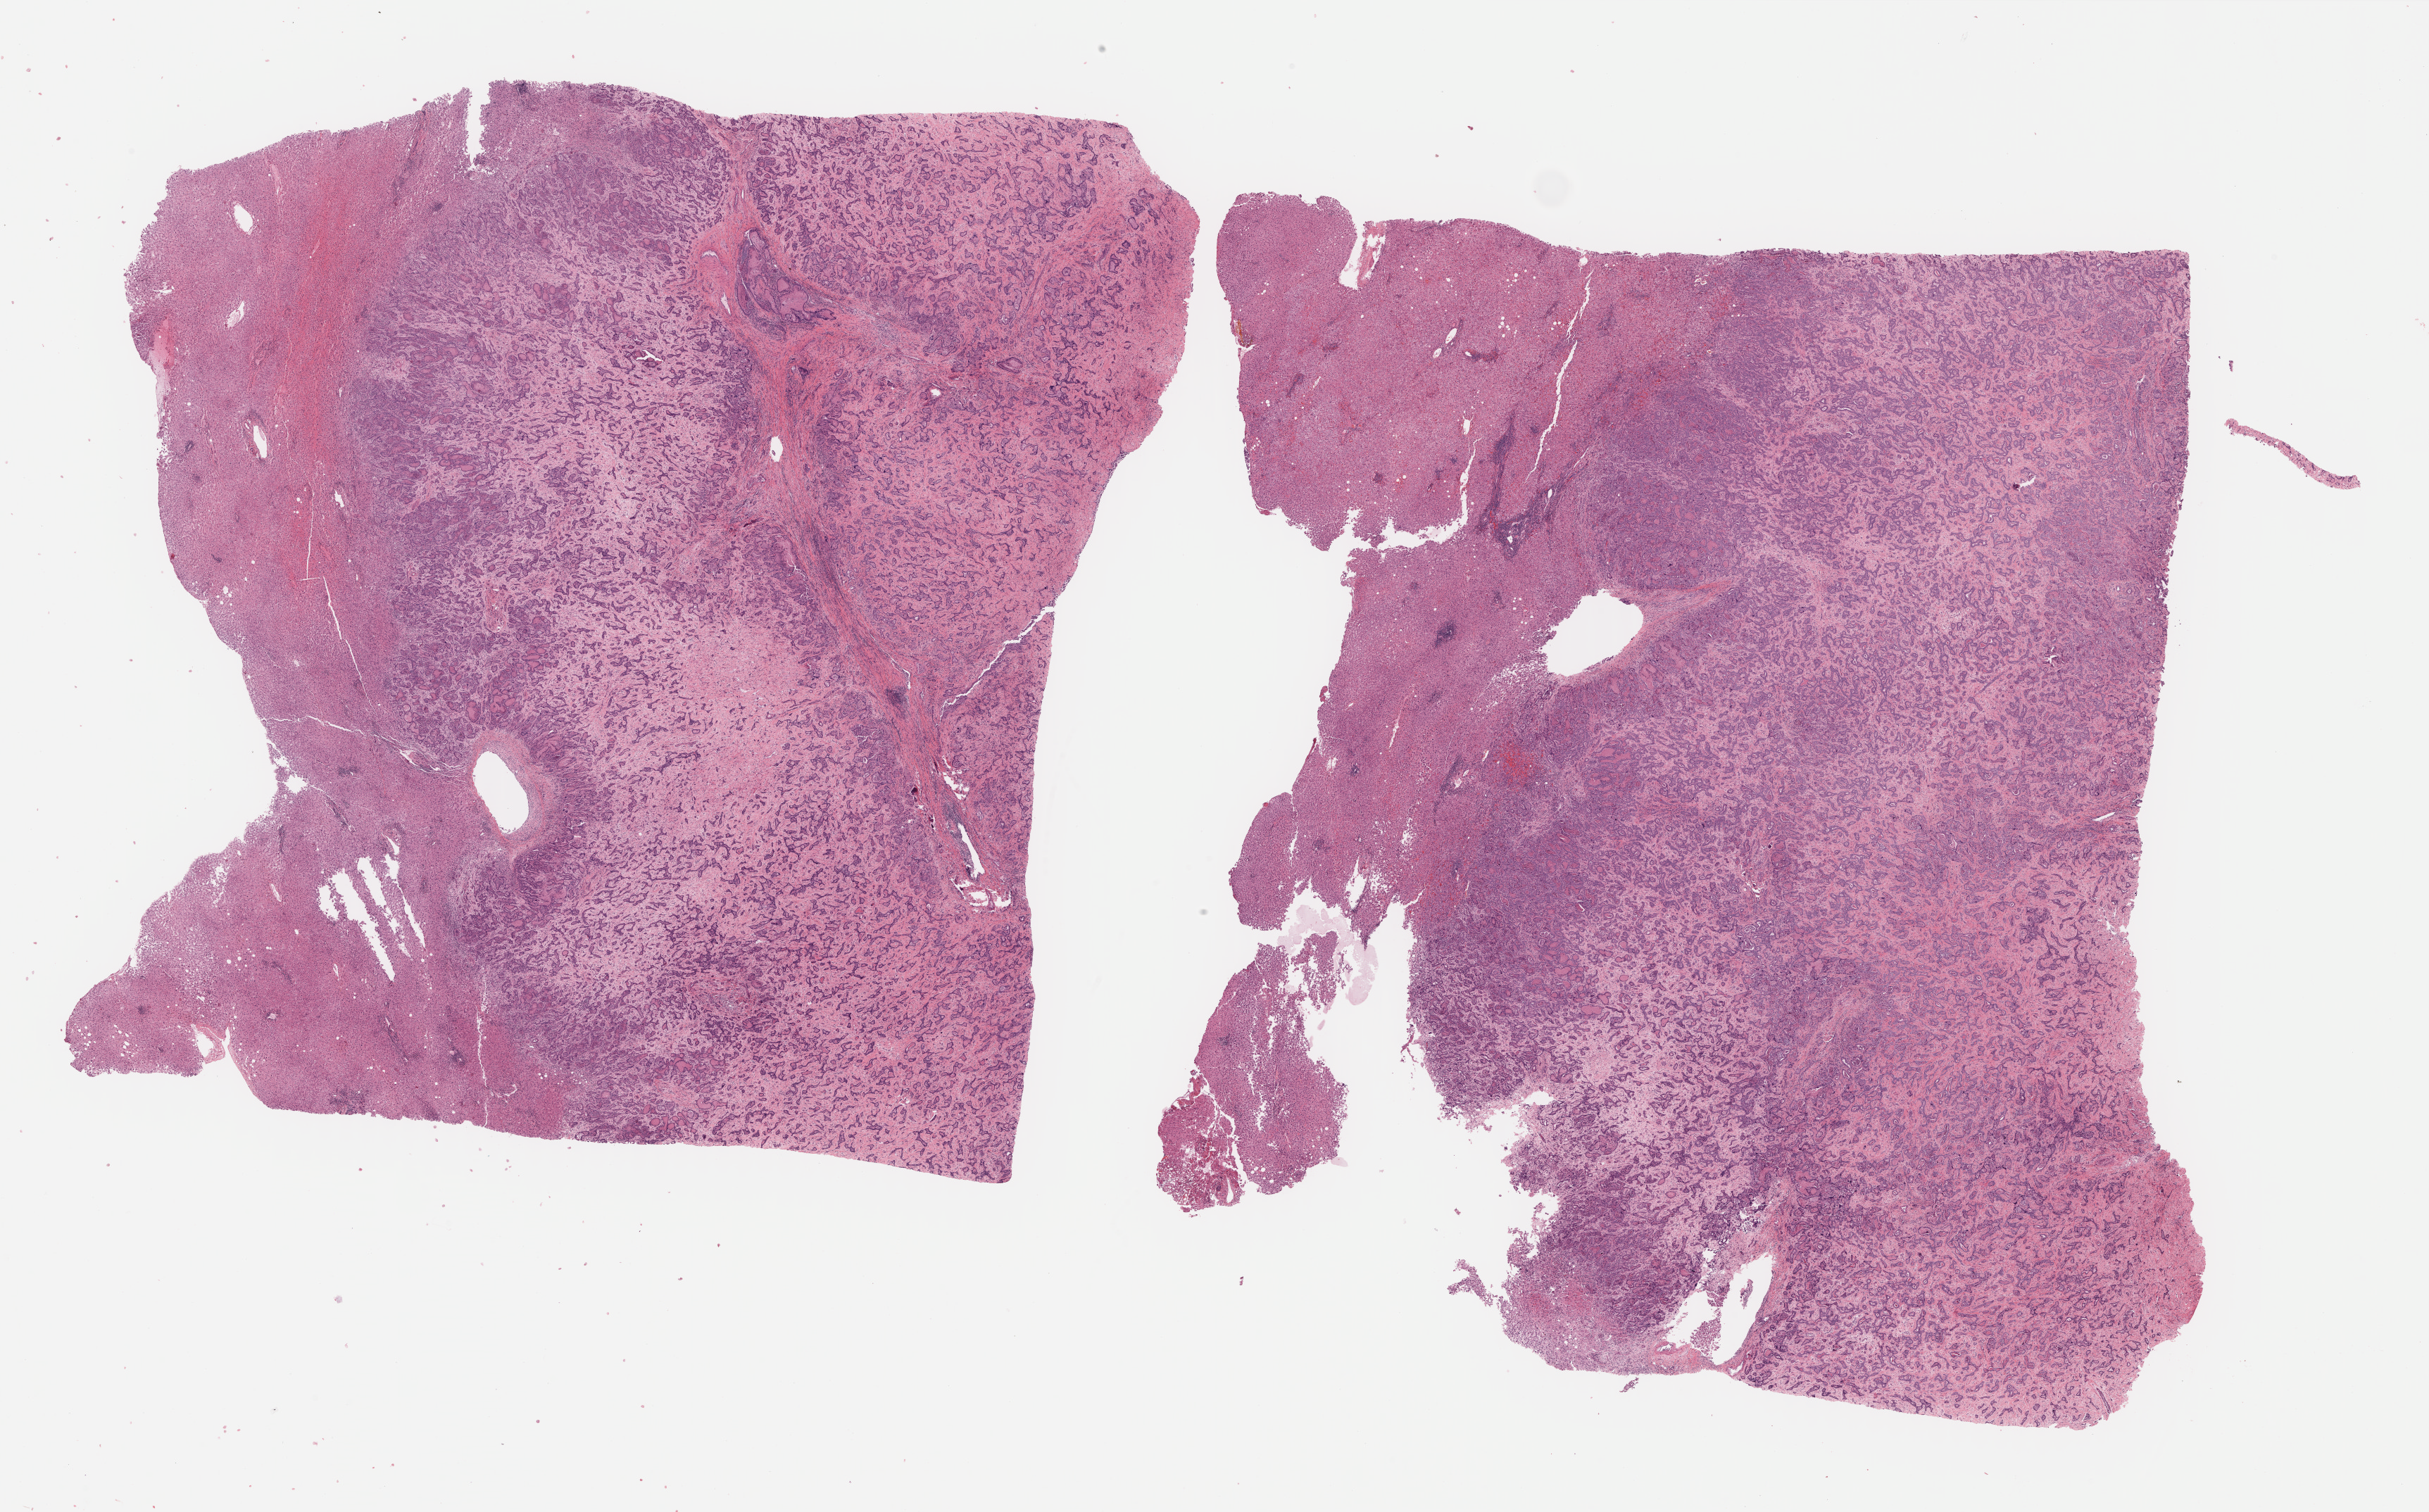
H&E whole-slide image — shown as a low-resolution overview of the whole scanned area (about 27.9 x 17.4 mm); formalin-fixed paraffin-embedded (FFPE) diagnostic section; primary tumour sample from the bile duct. Patient: male, age at initial diagnosis 66 years. Histologic grade: G2 (moderately differentiated).
- pathologic diagnosis: Cholangiocarcinoma (intrahepatic bile duct)
- AJCC pathologic stage: I (6th edition)